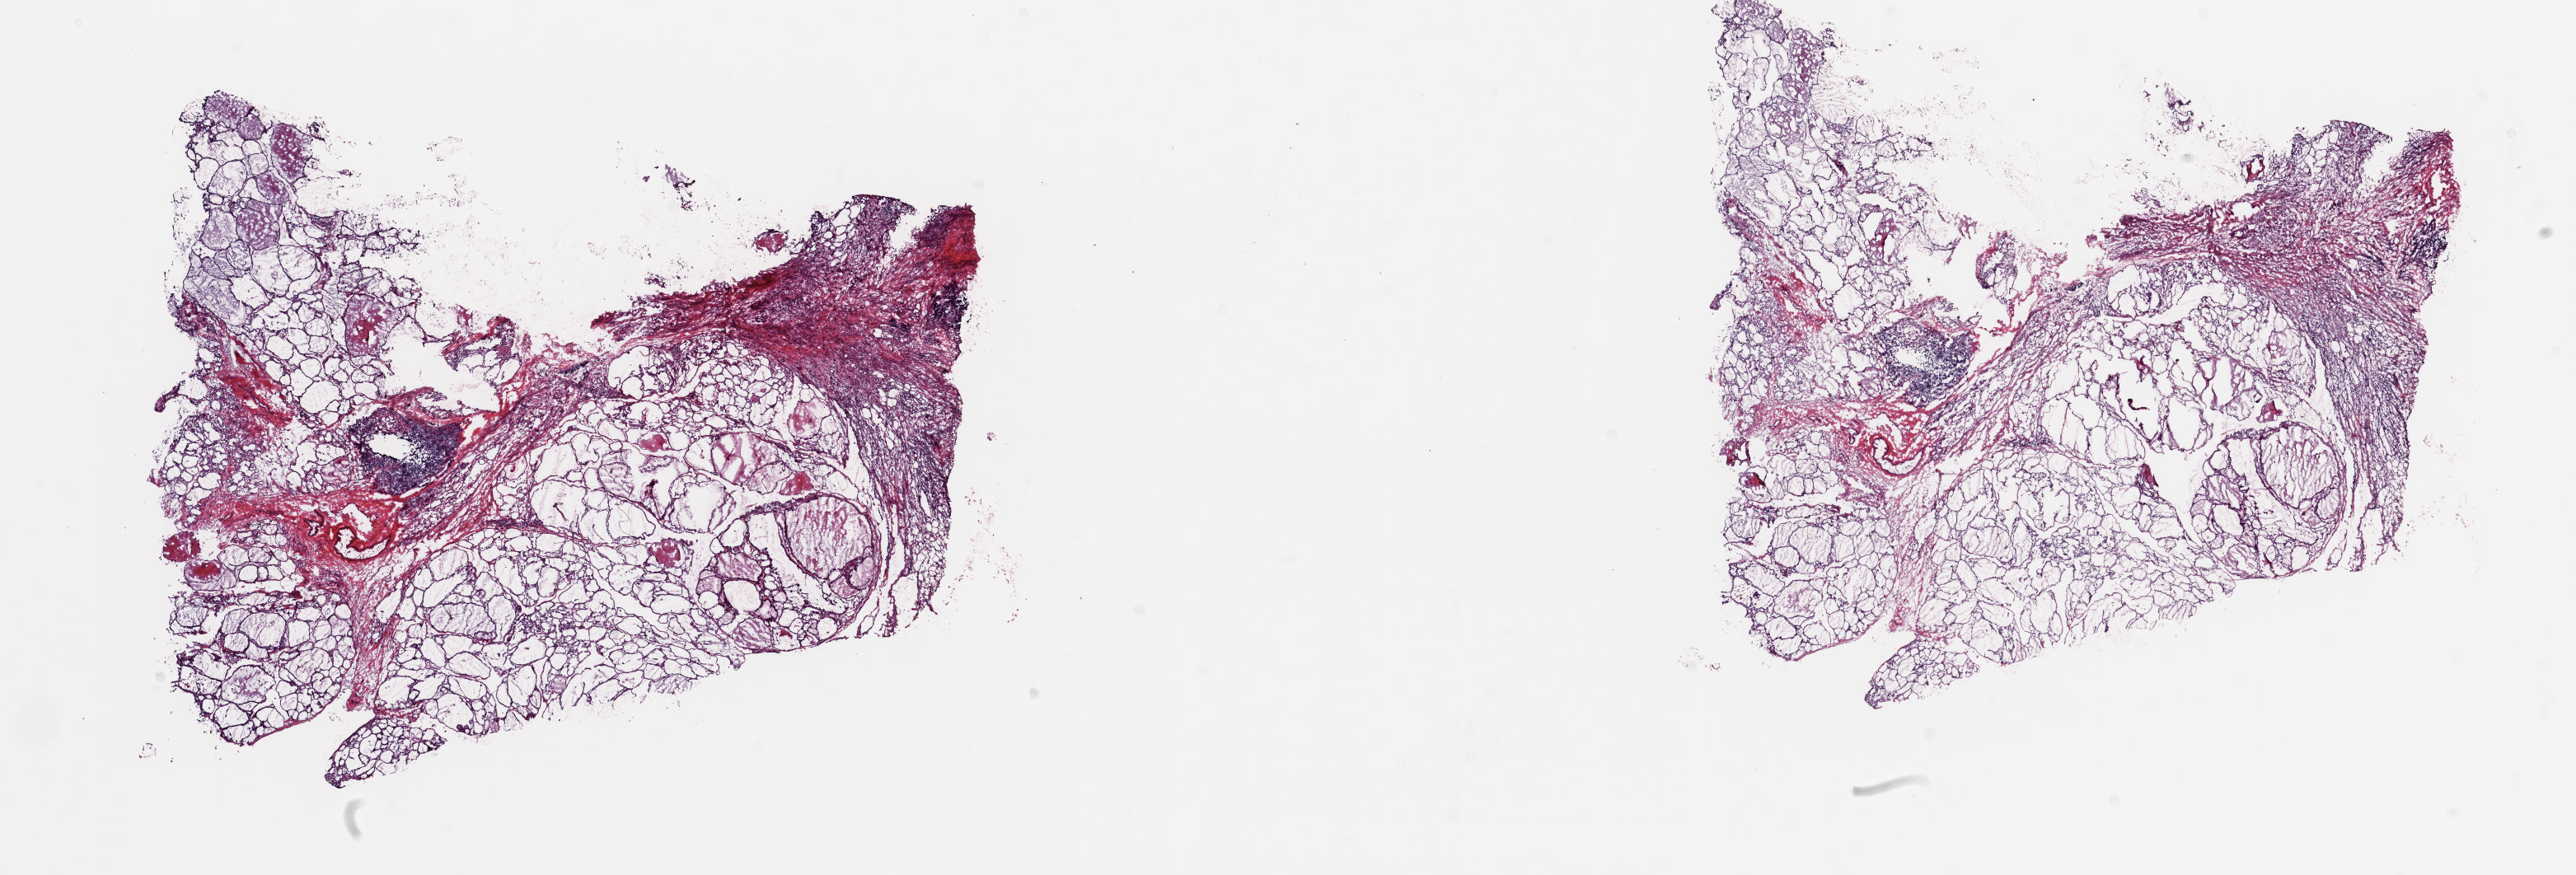
H&E-stained whole-slide image — shown as a low-resolution overview of the whole scanned area (about 24.8 x 8.4 mm, slide scanned at 20x), frozen section from the top of the tissue portion, sample: solid tissue normal (non-tumour tissue), thyroid. Patient: female, age at initial diagnosis 38 years. Composition of this section per pathologist review: tumour cells 0%, tumour nuclei 0%, normal cells 70%, stromal cells 30%, necrosis 0%. Infiltration values recorded for this section: lymphocyte infiltration 10%, monocyte infiltration 0%, neutrophil infiltration 0%.
This section: solid tissue normal (non-tumour) sample from the same patient. Patient diagnosis: Papillary adenocarcinoma, NOS (thyroid gland).